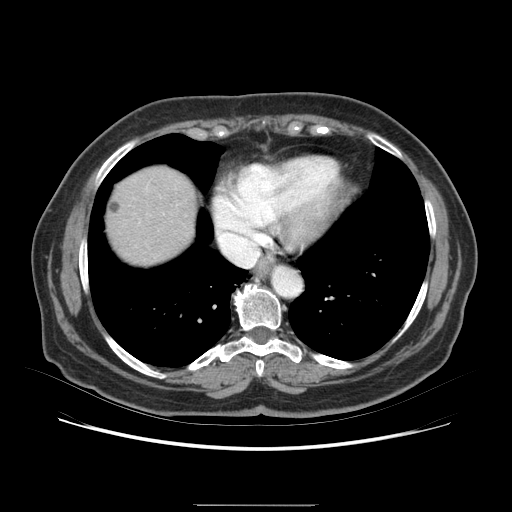
Contrast-enhanced abdominal CT (liver protocol), one axial slice. Slice 74 of 79 in the series (ordered by position). 120 kVp. Soft-tissue window (W 400 / L 40 HU). 2.5 mm slice thickness. 512 × 512 image matrix, field of view 380 × 380 mm. Case-level facts recorded for this patient, not image findings: diagnosis: hepatocellular carcinoma (patient treated with transarterial chemoembolisation; whether this scan precedes or follows treatment is not stated here); TNM stage (as recorded): Stage-I.
Annotated regions visible in this slice (semi-automatic segmentation, software-assisted and operator-edited):
- liver parenchyma outside the tumour (the mass and vessels are separate outlines, so this box may not span the whole liver): bounding box [x1, y1, x2, y2] px = [134, 182, 177, 224]